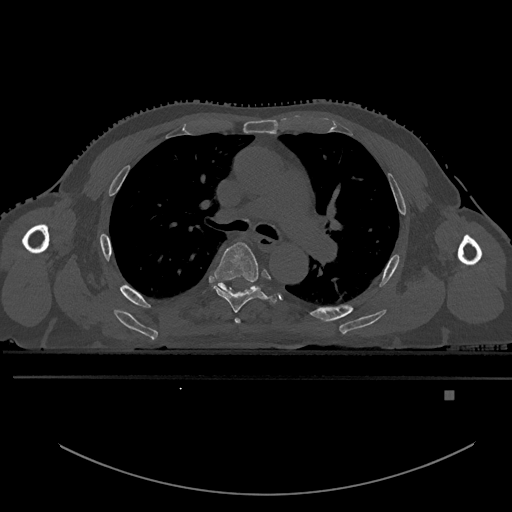
CT including the spine, one axial slice. Position 354 of 969 along the scan axis. Bone window (W 1800 / L 400 HU). 512 × 512 image matrix, field of view 456 × 456 mm. Male patient, age 82 years. From the clinical record (not read from this slice): primary cancer: prostate; vertebrae with lytic lesions (as recorded): T11, T9, T8, T2.
Annotated regions visible in this slice (semi-automatic segmentation, software-assisted and operator-edited):
- T4 vertebra: bounding box (x1, y1, x2, y2) in pixels: (235, 318, 241, 324)
- T5 vertebra: (213, 241, 278, 313)
- T6 vertebra: (212, 283, 251, 292)